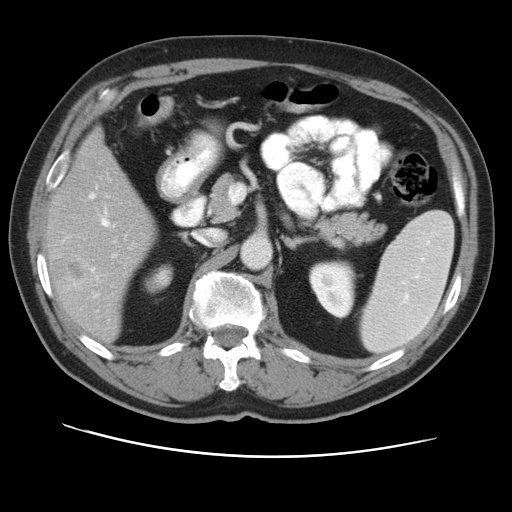
Contrast-enhanced abdominal CT, one axial slice; position 24 of 49 along the scan axis; reconstruction kernel STANDARD; 120 kVp; intravenous contrast given; soft-tissue window (W 400 / L 40 HU); 5 mm slice thickness; 512 × 512 image matrix, field of view 374 × 374 mm. Male patient, age 59 years. Case-level facts recorded for this patient, not image findings: diagnosis: colorectal cancer liver metastases, imaged before liver resection; multiple liver metastases: yes; largest metastasis: 6.3 cm; disease in both lobes: yes.
Outlined on this slice (expert manual segmentation):
- hepatic veins: box from (x=90, y=193) to (x=94, y=198) px
- liver: (x=47, y=134)–(x=154, y=340)
- planned liver remnant (the part of the liver to remain after resection): (x=51, y=134)–(x=154, y=340)
- portal vein (with intrahepatic branches): (x=92, y=209)–(x=115, y=296)
- liver metastasis: (x=54, y=242)–(x=87, y=279)